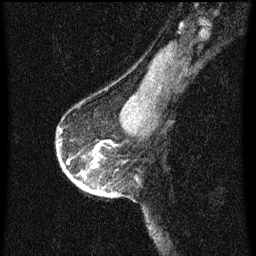
Breast MRI (dynamic contrast-enhanced), one sagittal slice; slice 47 of 60 in the series (ordered by position); dynamic contrast-enhanced series, image 2 of 3 at this slice position (ordered by acquisition); 1.5 T; TE 4.2 ms, TR 8 ms; 2 mm slice thickness; 256 × 256 image matrix, field of view 180 × 180 mm. Patient: female, 56 years.
Outlined on this slice (semi-automatic segmentation, software-assisted and operator-edited):
- analysis volume of interest (the breast-tissue region the enhancement analysis was run in; not a lesion): bounding box [x1, y1, x2, y2] px = [56, 128, 117, 199]
- tumour enhancement mask (voxels above the 70 % enhancement threshold inside the analysis volume of interest): [69, 146, 116, 197]